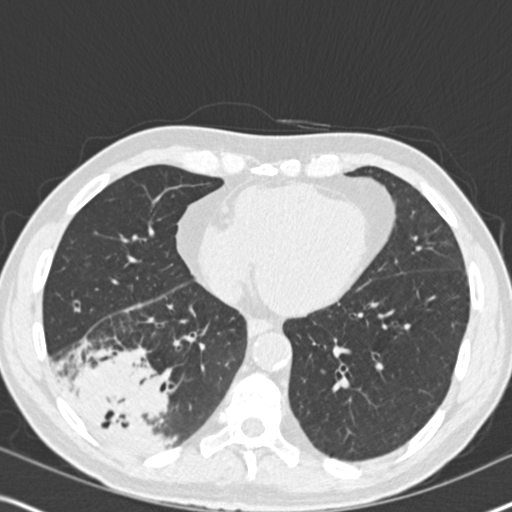
Low-dose screening chest CT, one axial slice. Position 72 of 182 along the scan axis. Lung window (W 1500 / L -600 HU). 2 mm slice thickness. 512 × 512 image matrix, field of view 330 × 330 mm.
Structures marked on this image (outlined manually by an expert reader):
- lesion 1 (tumor, lower lobe of right lung): bounding box <66,350,171,459> (left, top, right, bottom; pixels)